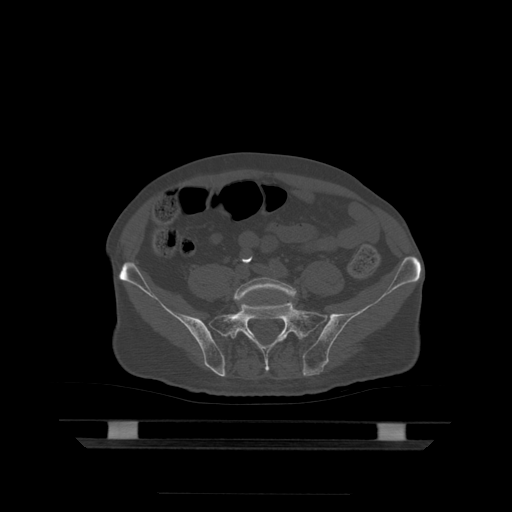
CT including the spine, one axial slice. Position 59 of 522 along the scan axis. Bone window (W 1800 / L 400 HU). 1.25 mm slice thickness. 512 × 512 image matrix, field of view 436 × 436 mm. Patient age 68 years. Case-level facts recorded for this patient, not image findings: primary cancer: urothelial.
Outlined on this slice (semi-automatic segmentation, software-assisted and operator-edited):
- L5 vertebra: bounding box (x1, y1, x2, y2) in pixels: (234, 278, 297, 304)